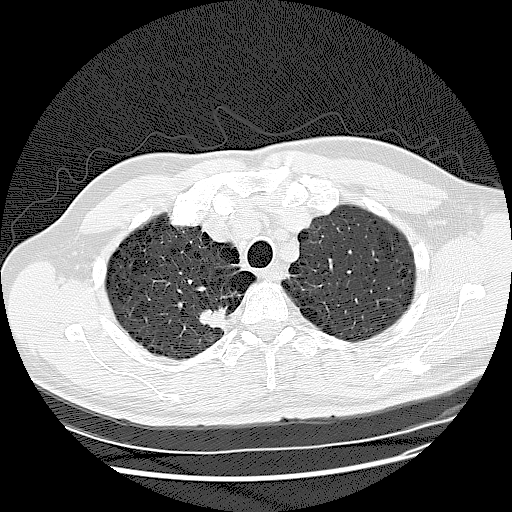
Low-dose screening chest CT, one axial slice. Position 109 of 132 along the scan axis. Reconstruction kernel LUNG. 120 kVp. Lung window (W 1500 / L -600 HU). 512 × 512 image matrix, field of view 380 × 380 mm.
Structures marked on this image (outlined manually by an expert reader):
- lesion 1 (tumor, upper lobe of right lung): bounding box [x1, y1, x2, y2] px = [200, 306, 229, 330]